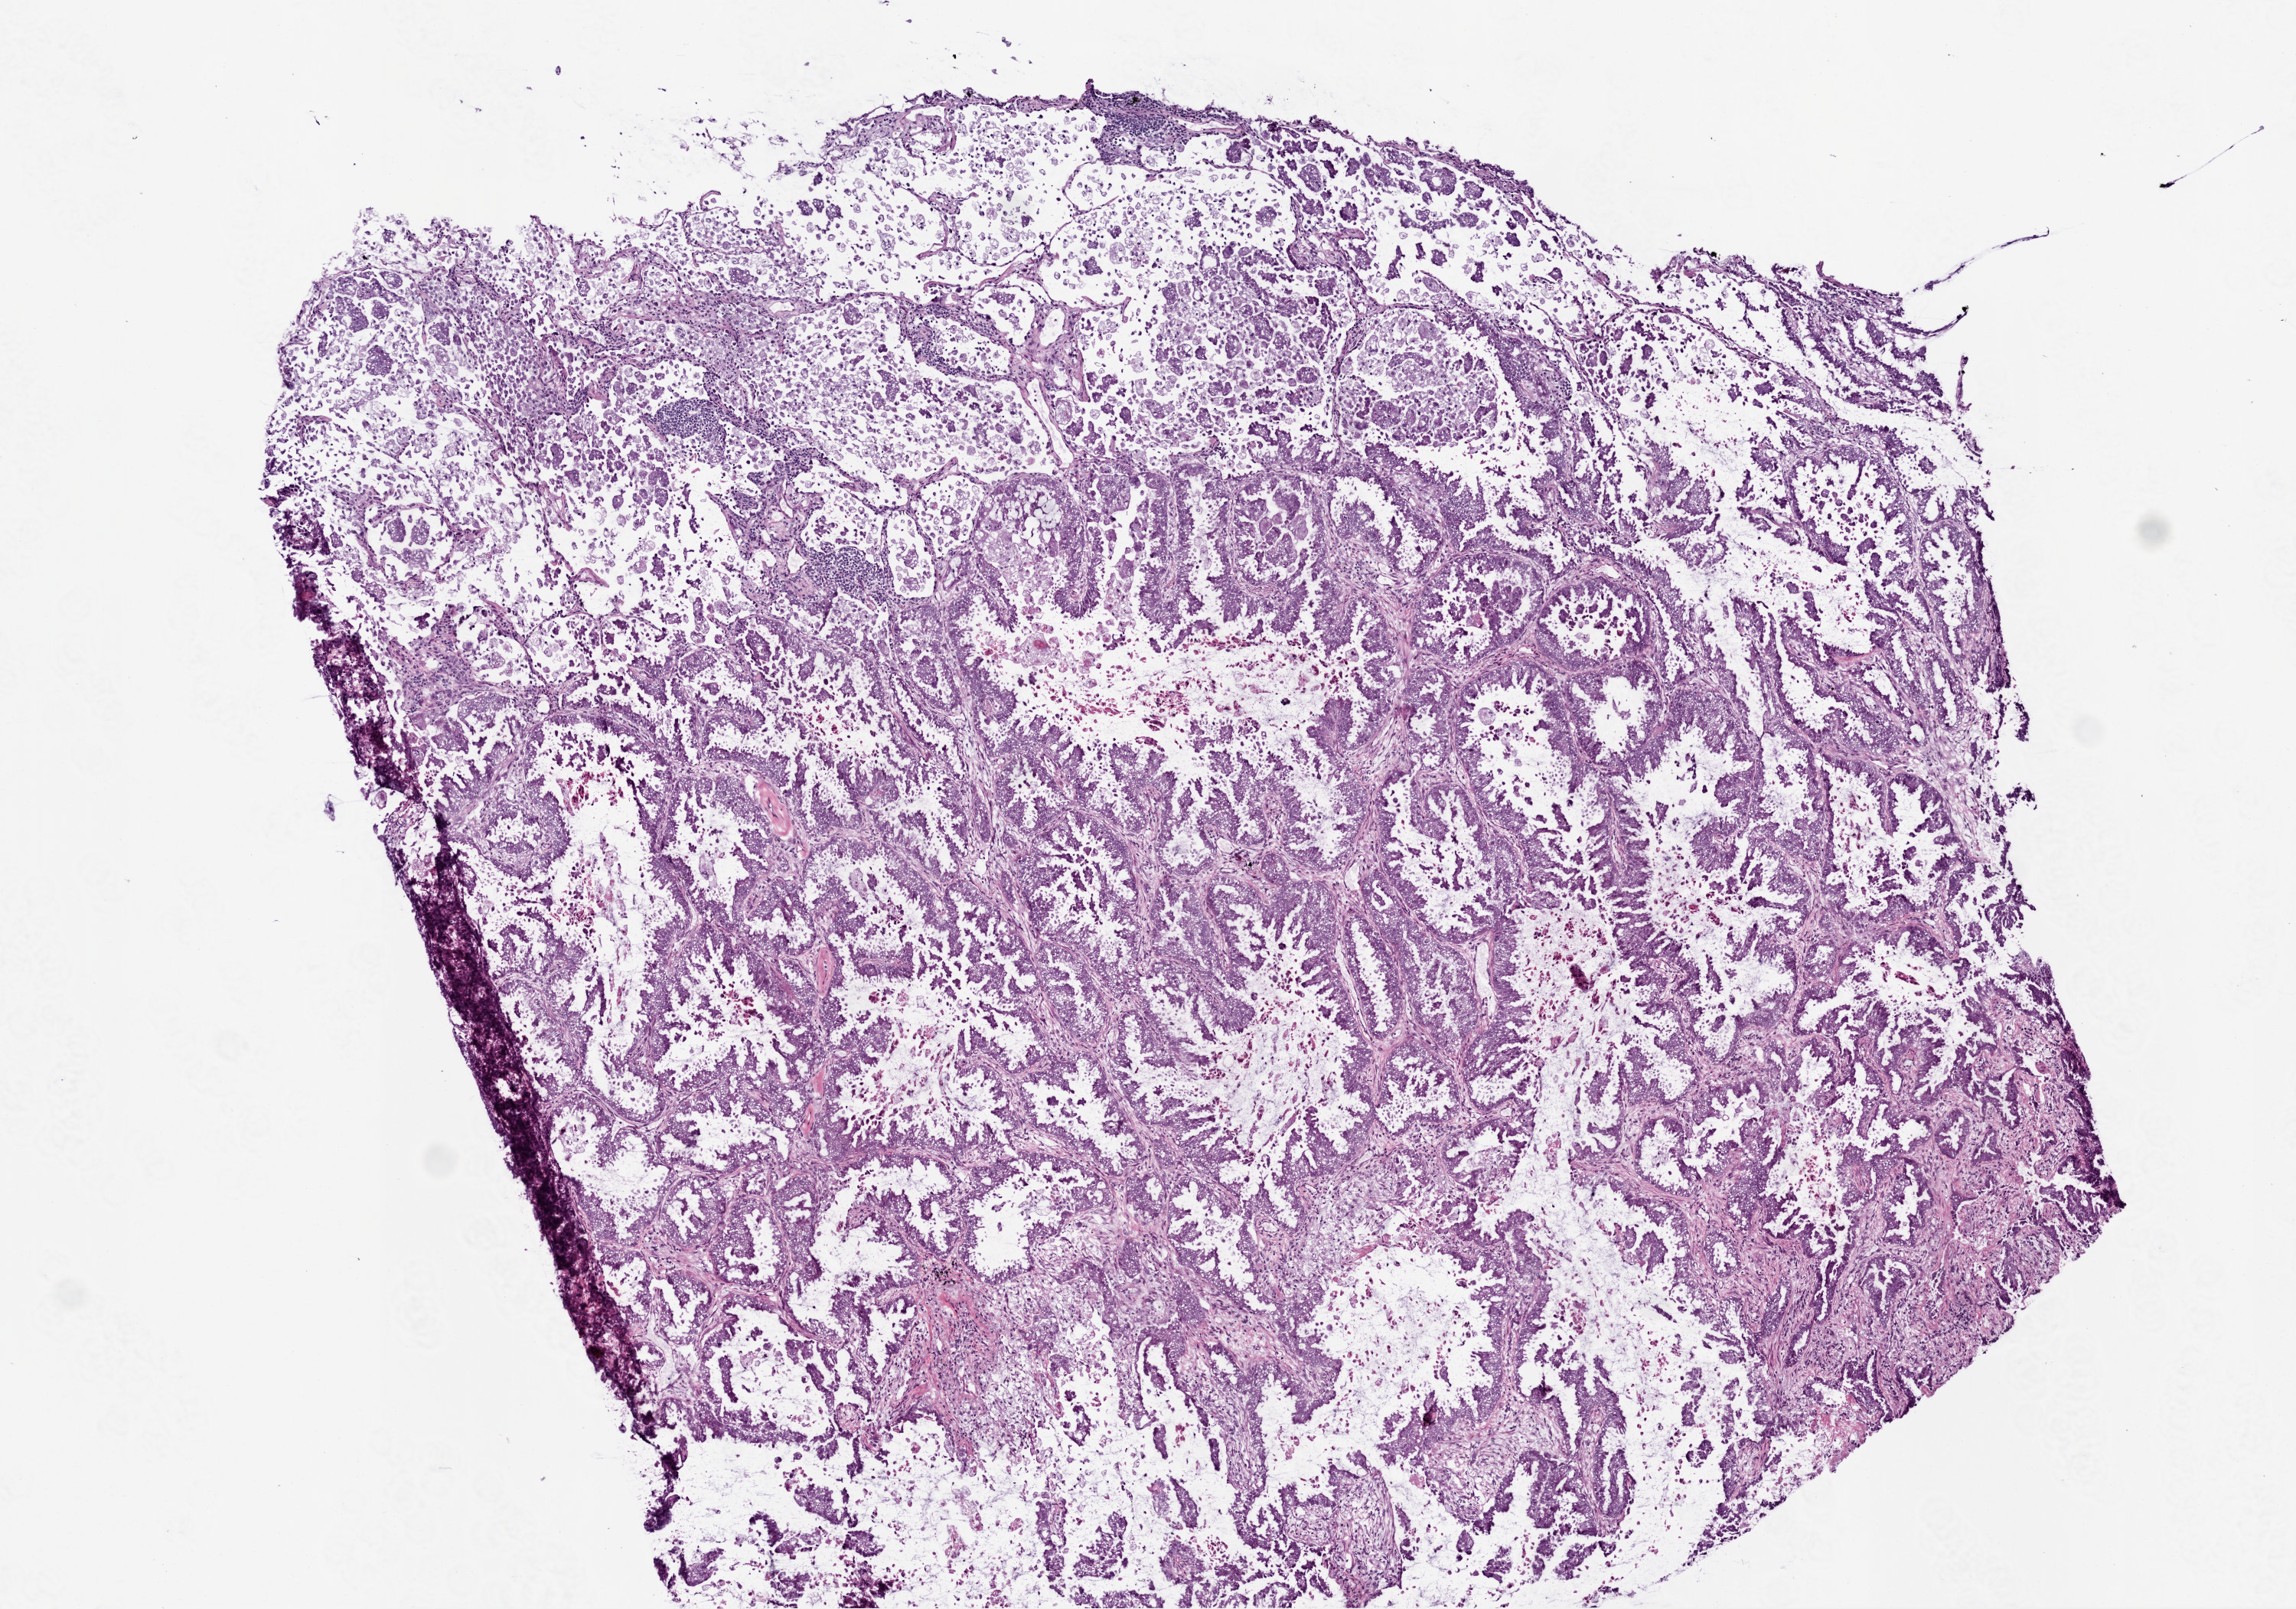
Whole-slide histology image, H&E — whole scanned area (about 6.0 x 4.2 mm, slide scanned at 20x) shown as a low-resolution overview, frozen section from the top of the tissue portion, lung, primary tumour sample. Female, age 69 years at initial diagnosis. Composition of this section per pathologist review: tumour cells 87%, tumour nuclei 70%.
Histologic diagnosis: Adenocarcinoma with mixed subtypes (upper lobe, lung).